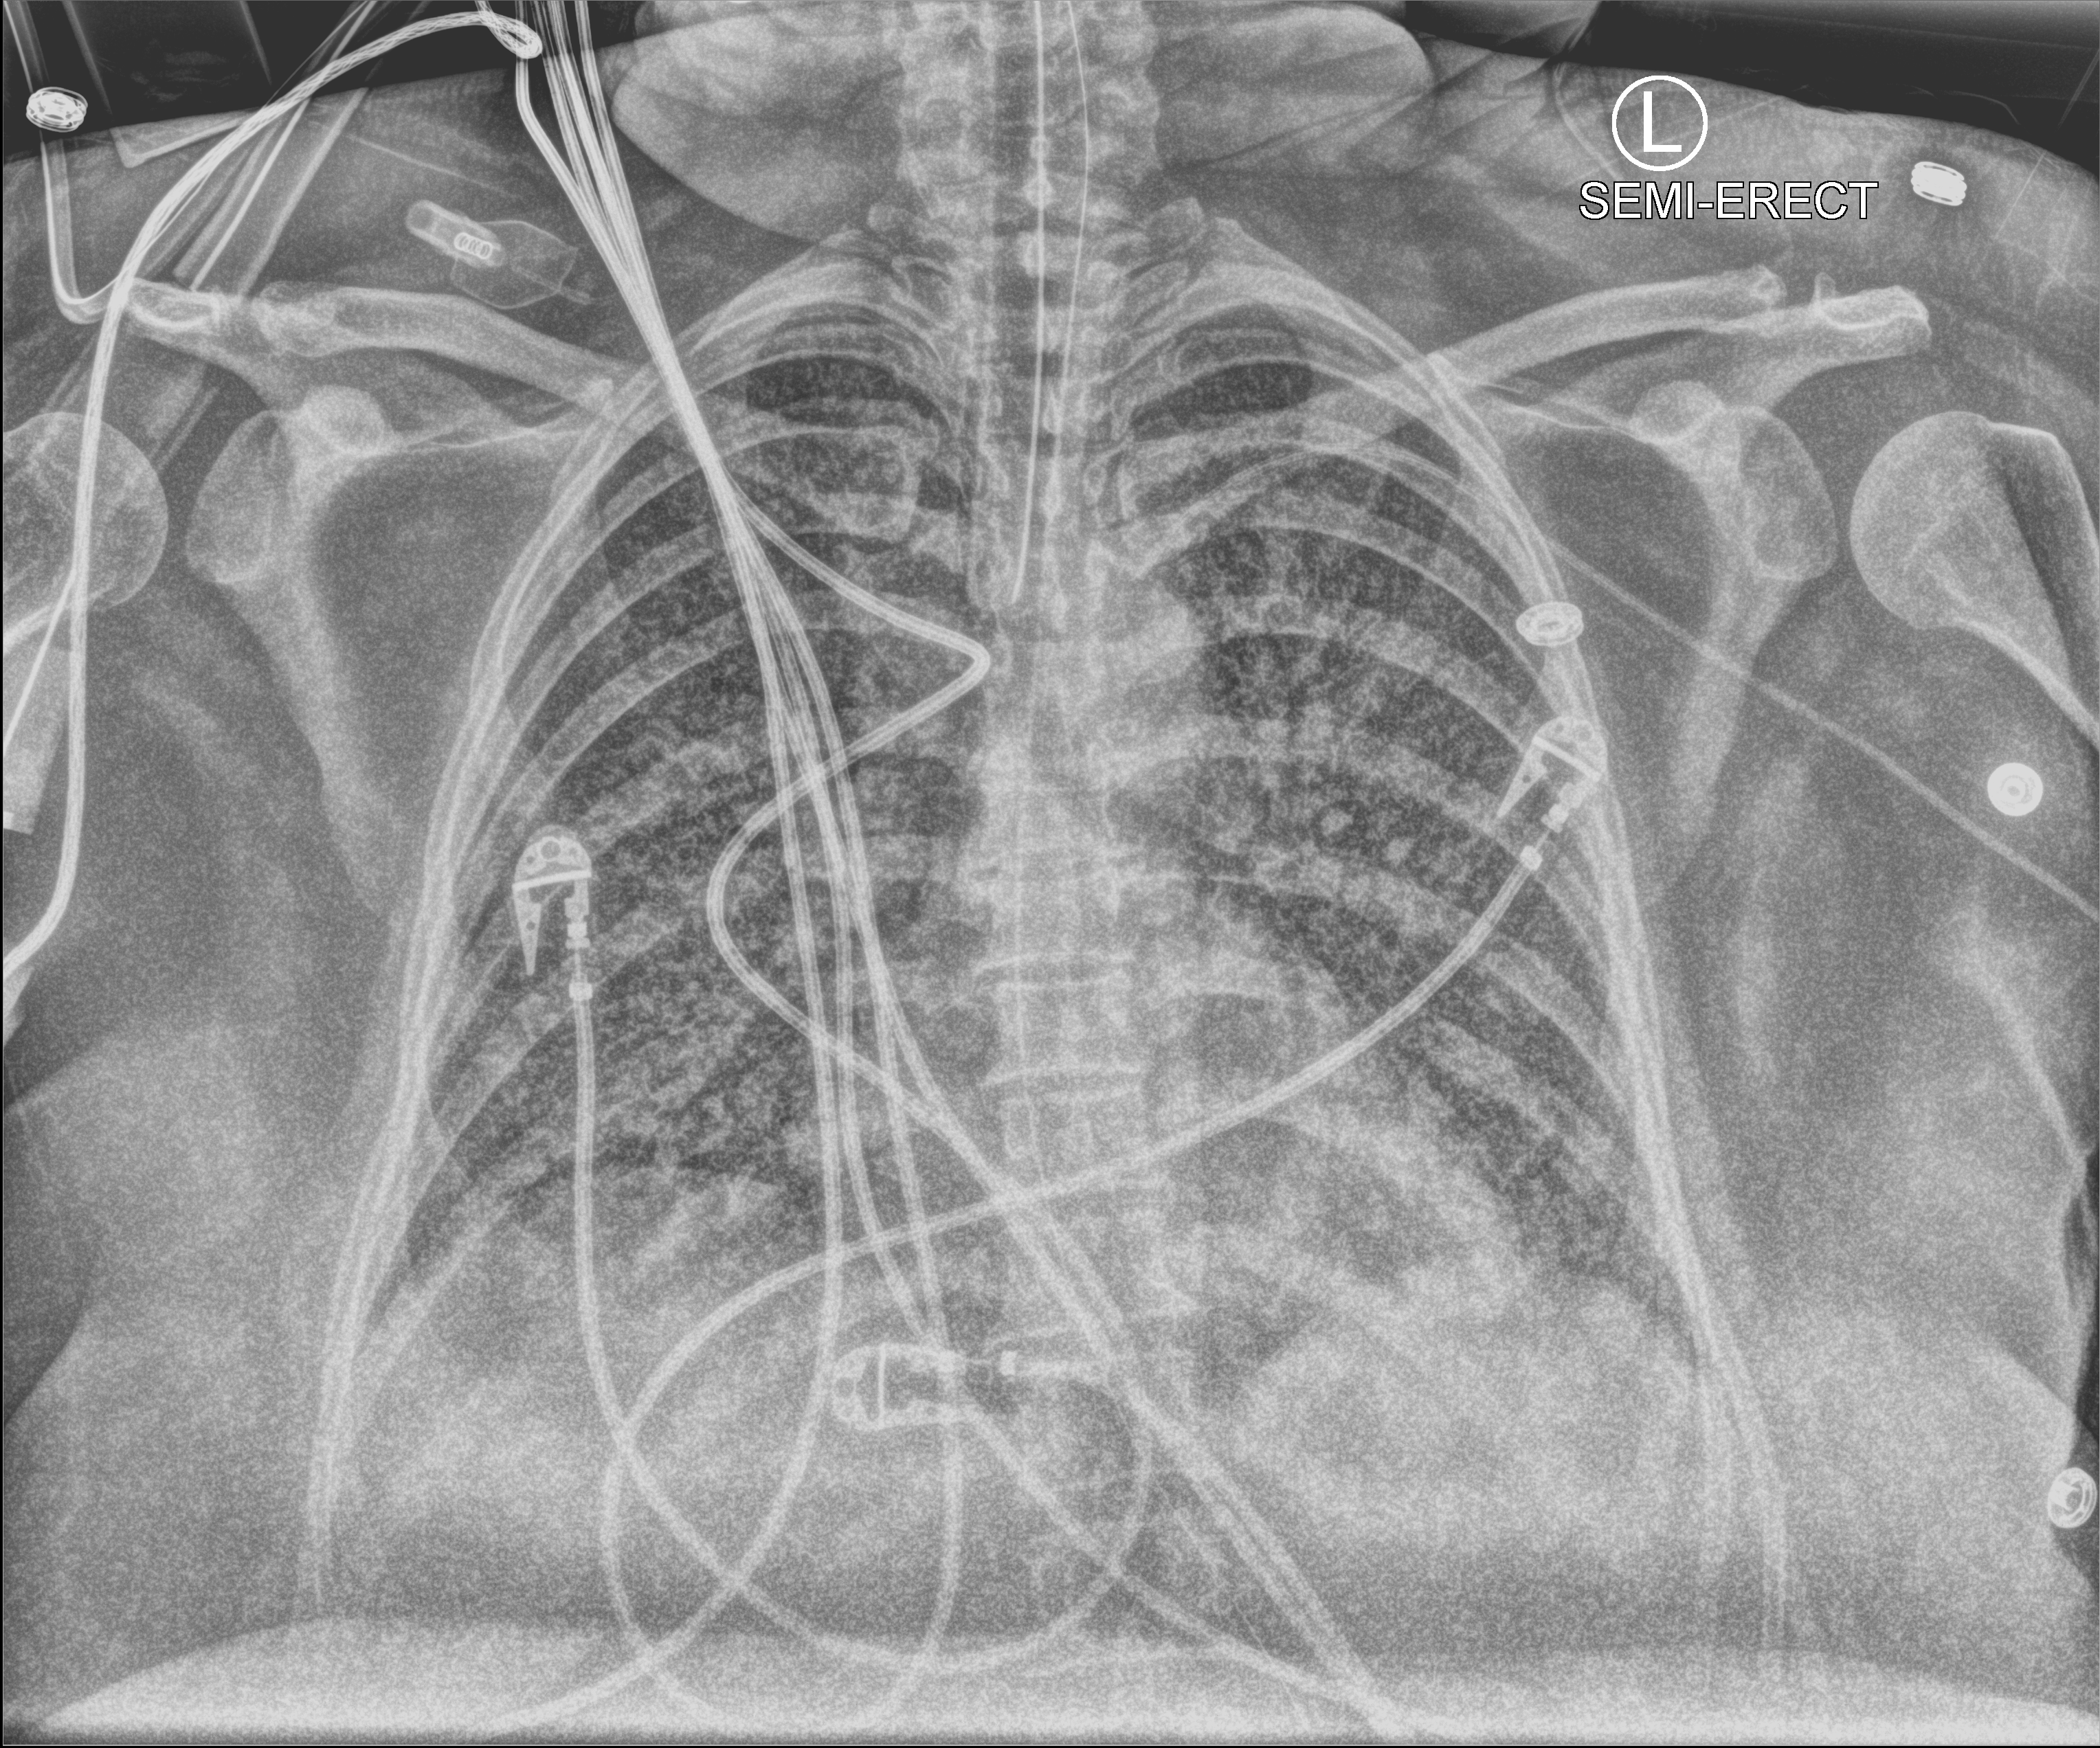
Chest X-ray (portable); anteroposterior (AP) projection. Patient hospitalised with COVID-19; female, aged 18–59 years.
Admission-level facts for this patient (not findings on this image; timing relative to this image not recorded):
- mechanically ventilated during this hospital stay: yes
- length of hospital stay: 95 days